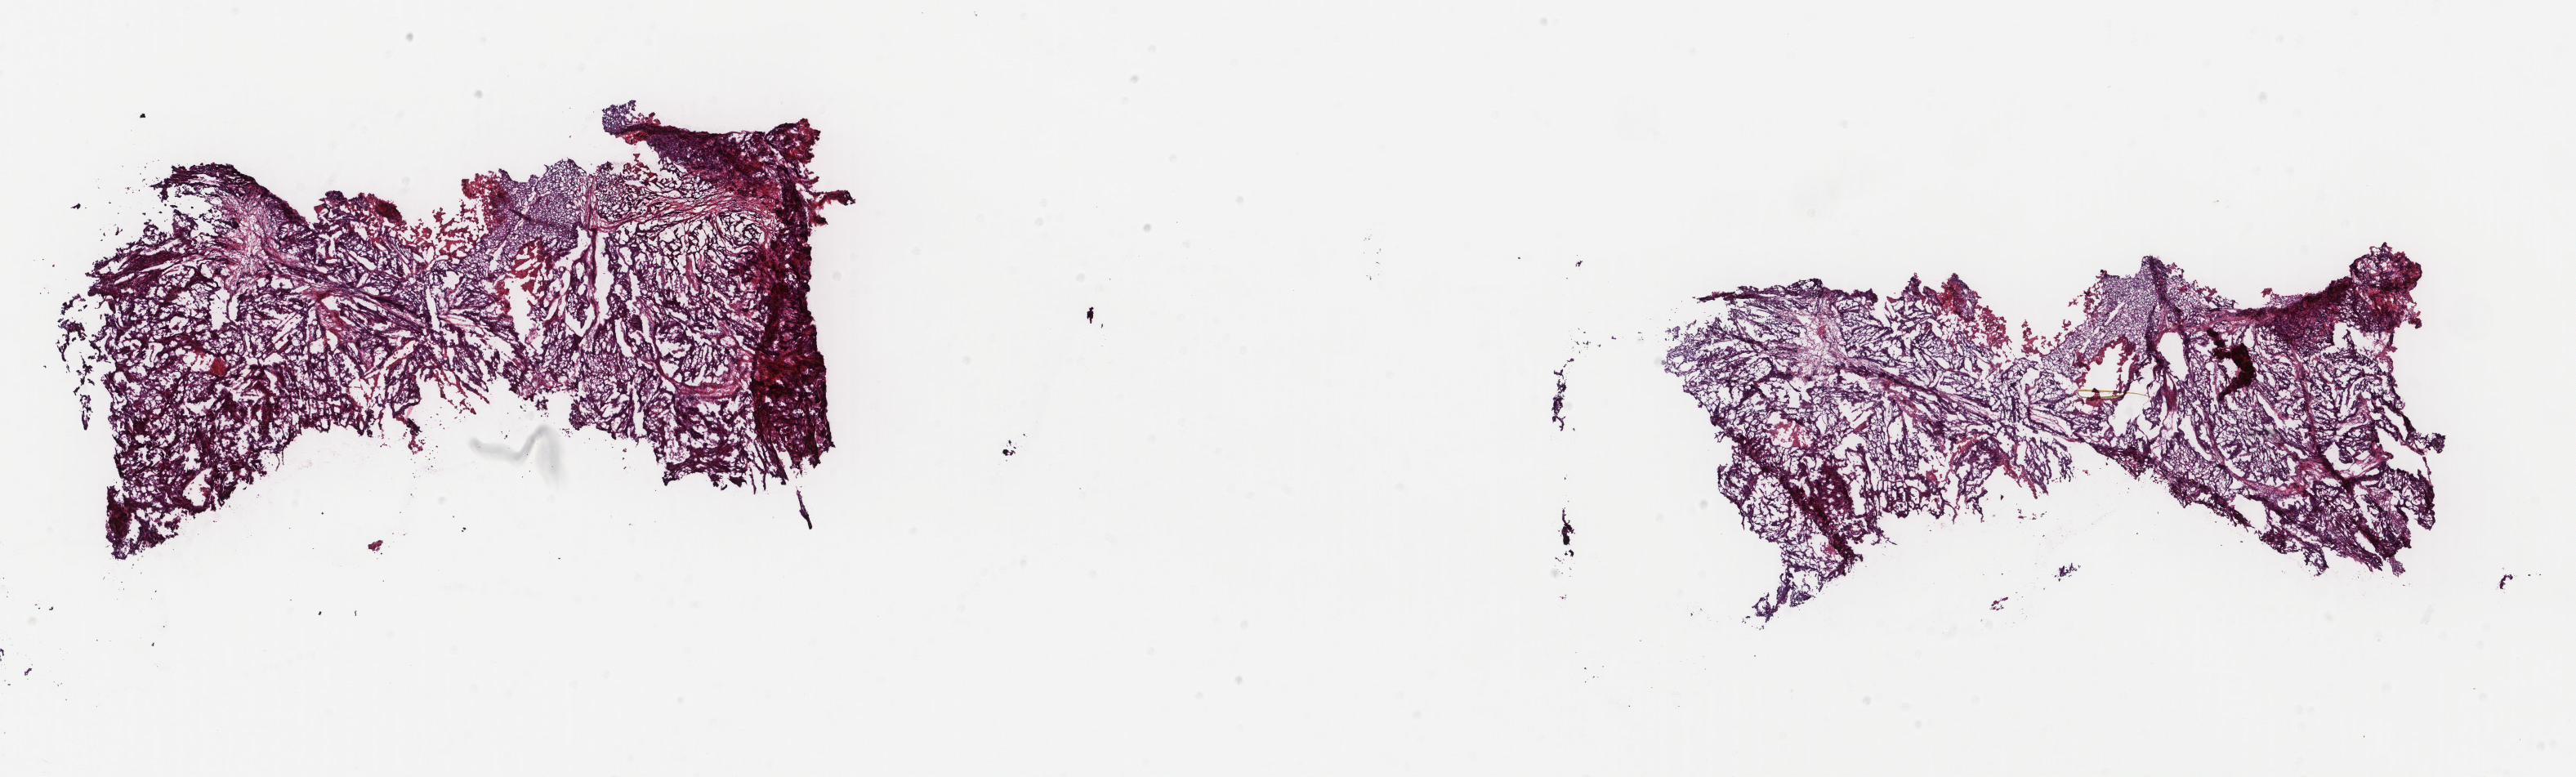
H&E whole-slide image — low-resolution overview of the scanned area, about 25.0 x 7.5 mm (from a 40x scan). Frozen section from the top of the tissue portion. Uterus, primary tumour sample. Female, age 60 years at initial diagnosis. Histologic grade: G3 (poorly differentiated). Composition of this section per pathologist review: tumour cells 82%, tumour nuclei 80%, normal cells 8%, stromal cells 2%, necrosis 8%. Infiltration values recorded for this section: lymphocyte infiltration 10%, monocyte infiltration 0%, neutrophil infiltration 0%.
Diagnosis: Endometrioid adenocarcinoma, NOS (endometrium). FIGO stage: IB.